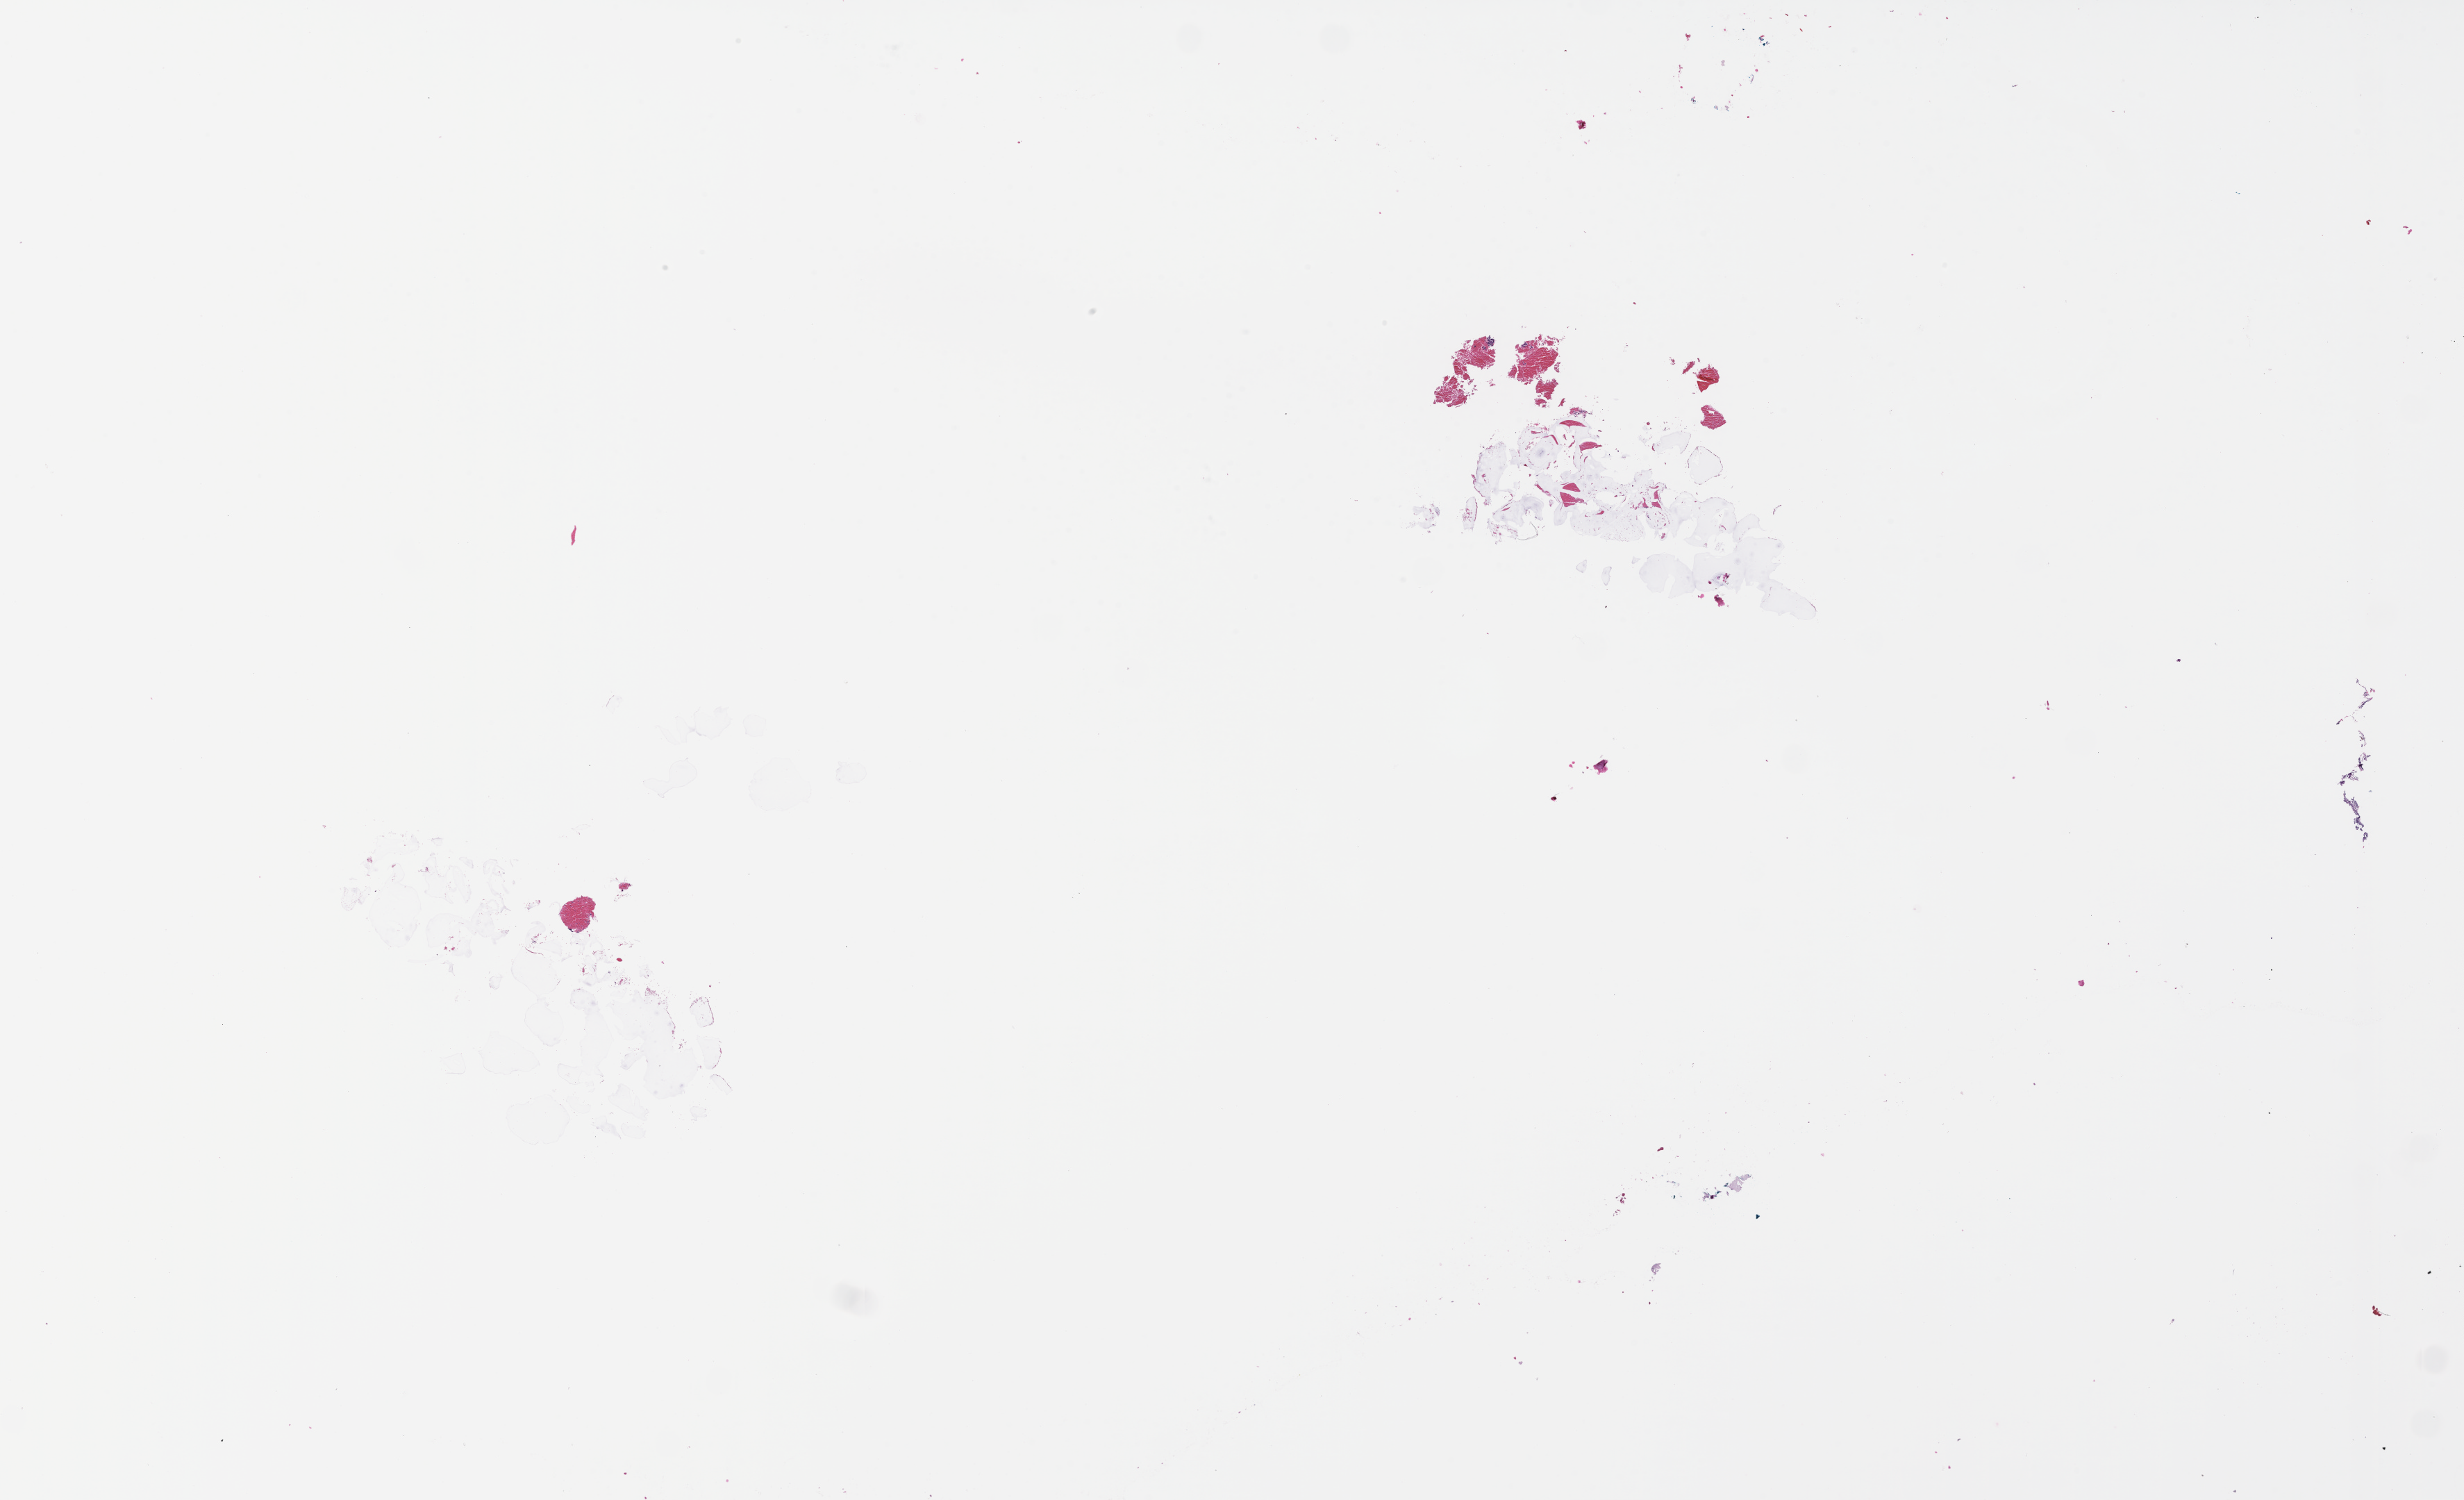
Hematoxylin and eosin (H&E) whole-slide image — low-resolution overview of the scanned area, about 28.6 x 17.4 mm. Formalin-fixed paraffin-embedded section. Specimen time point: archival tissue. Female patient.
* this section: metastatic tumor tissue
* patient diagnosis (primary): Non-Small Cell Lung Carcinoma